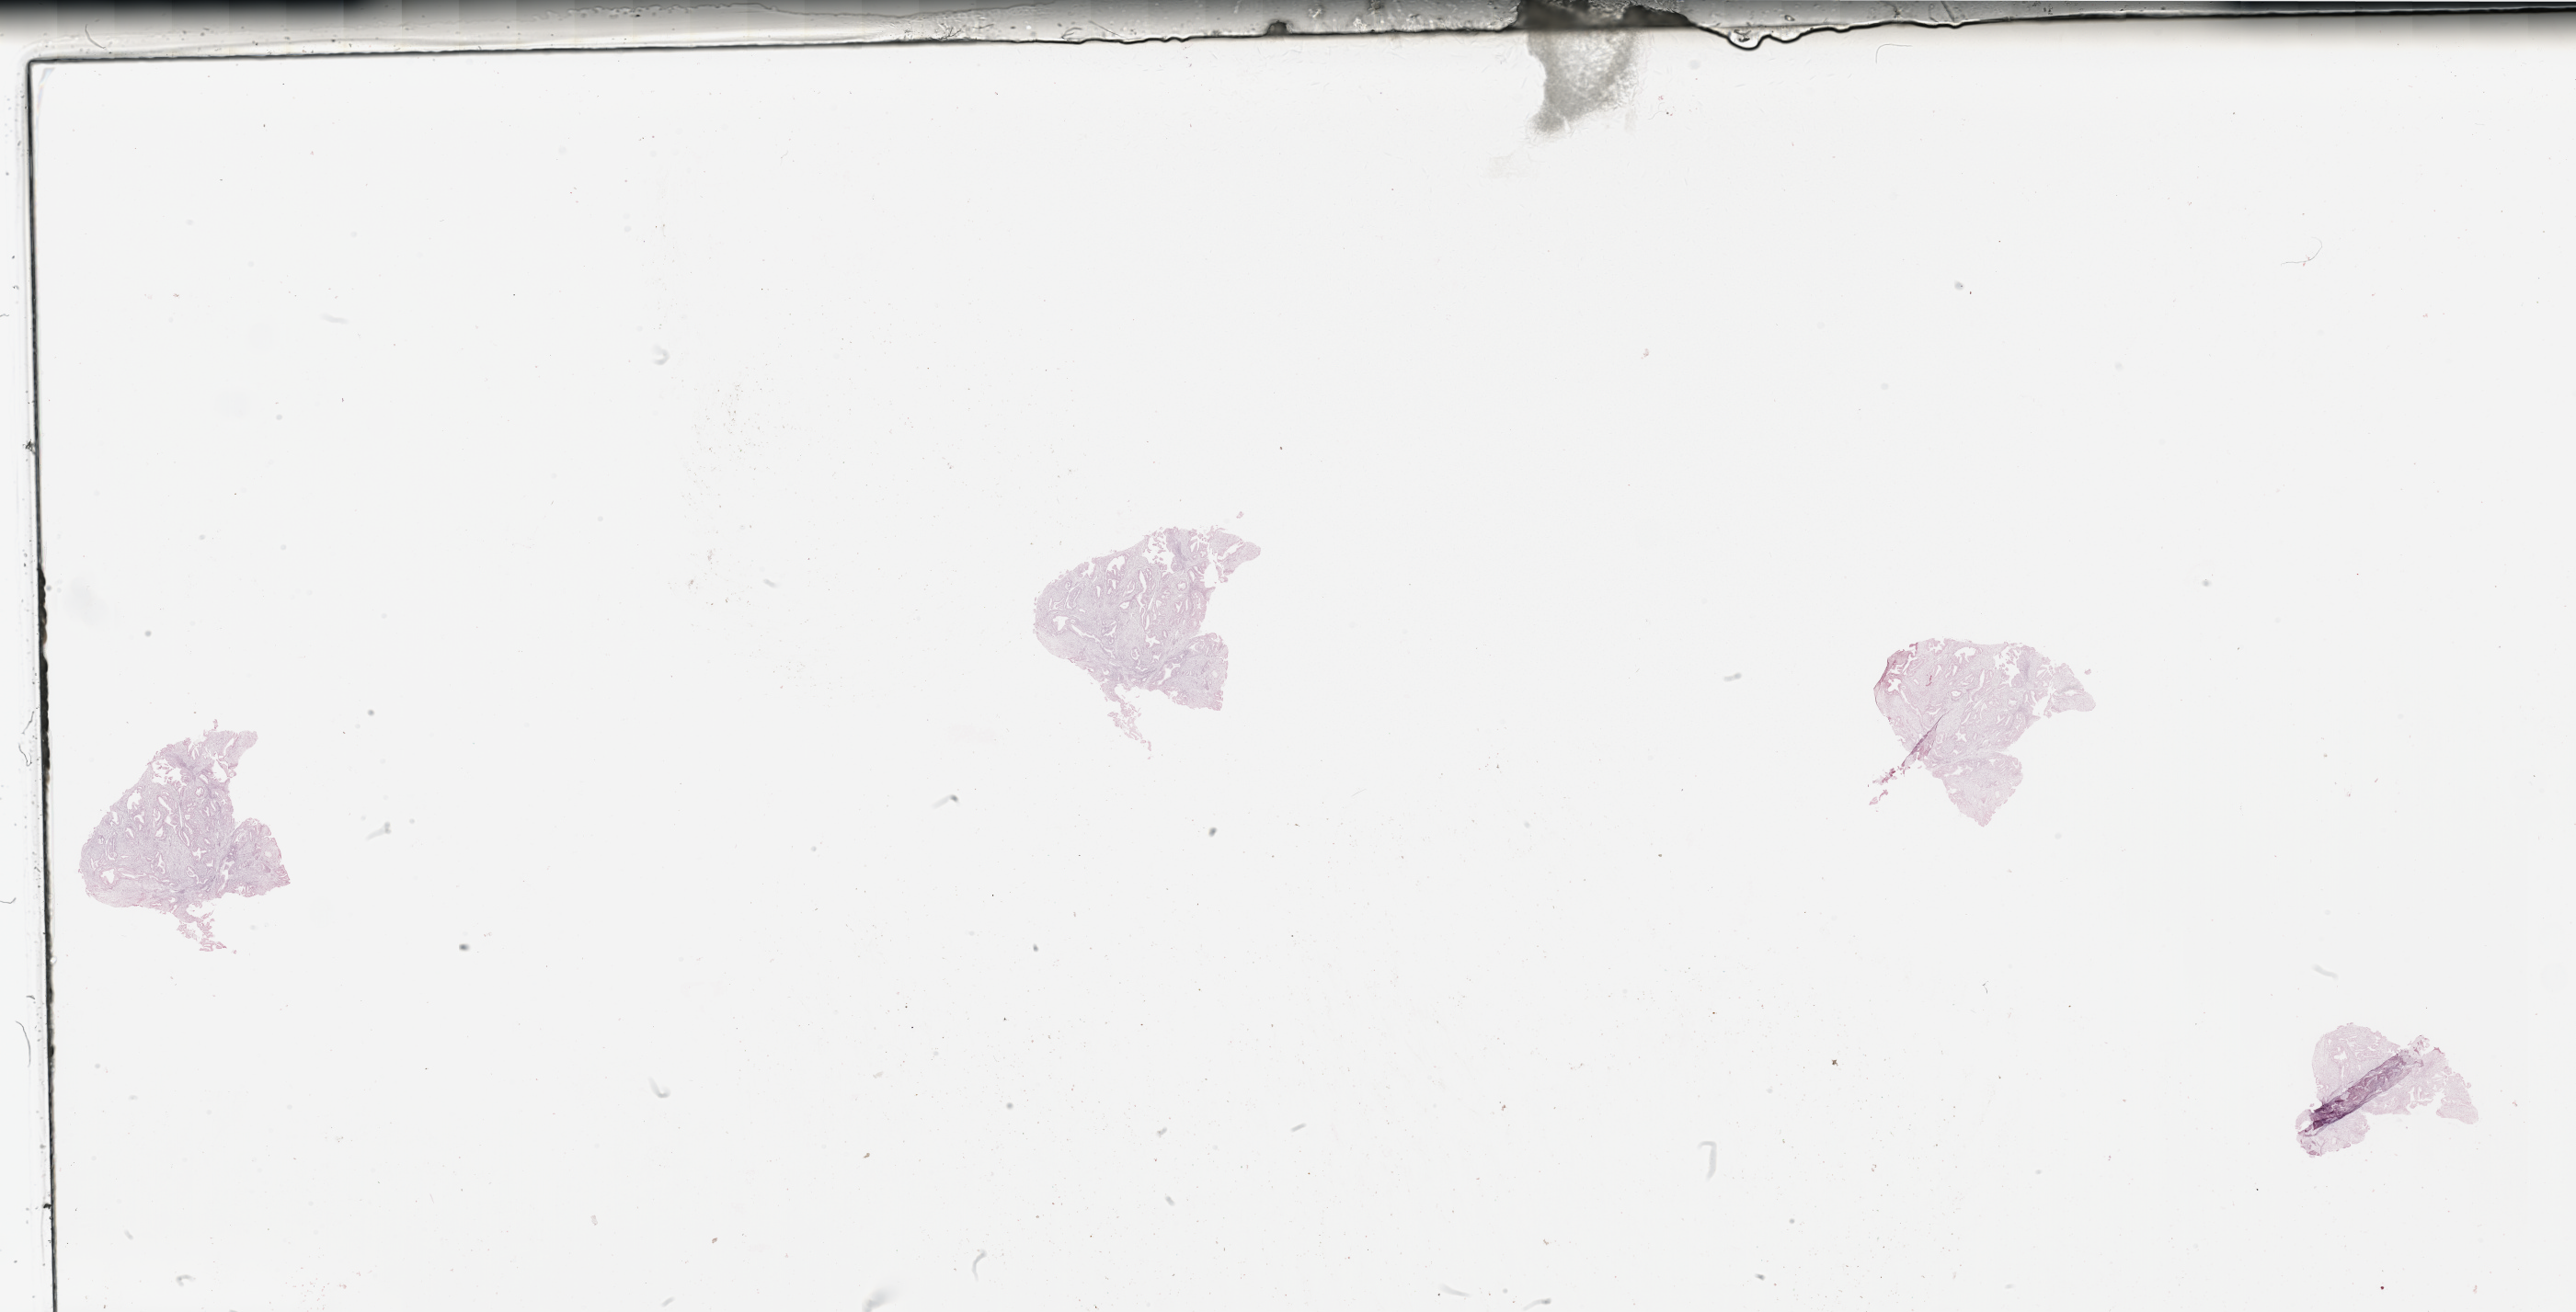
H&E whole-slide image — whole scanned area (about 44.3 x 22.6 mm) shown as a low-resolution overview. Tumour tissue sample, uterus. Patient: female, age 75 years. Histologic grade: G1 (well differentiated).
Diagnosis: Endometrioid adenocarcinoma, NOS. AJCC pathologic stage: I.